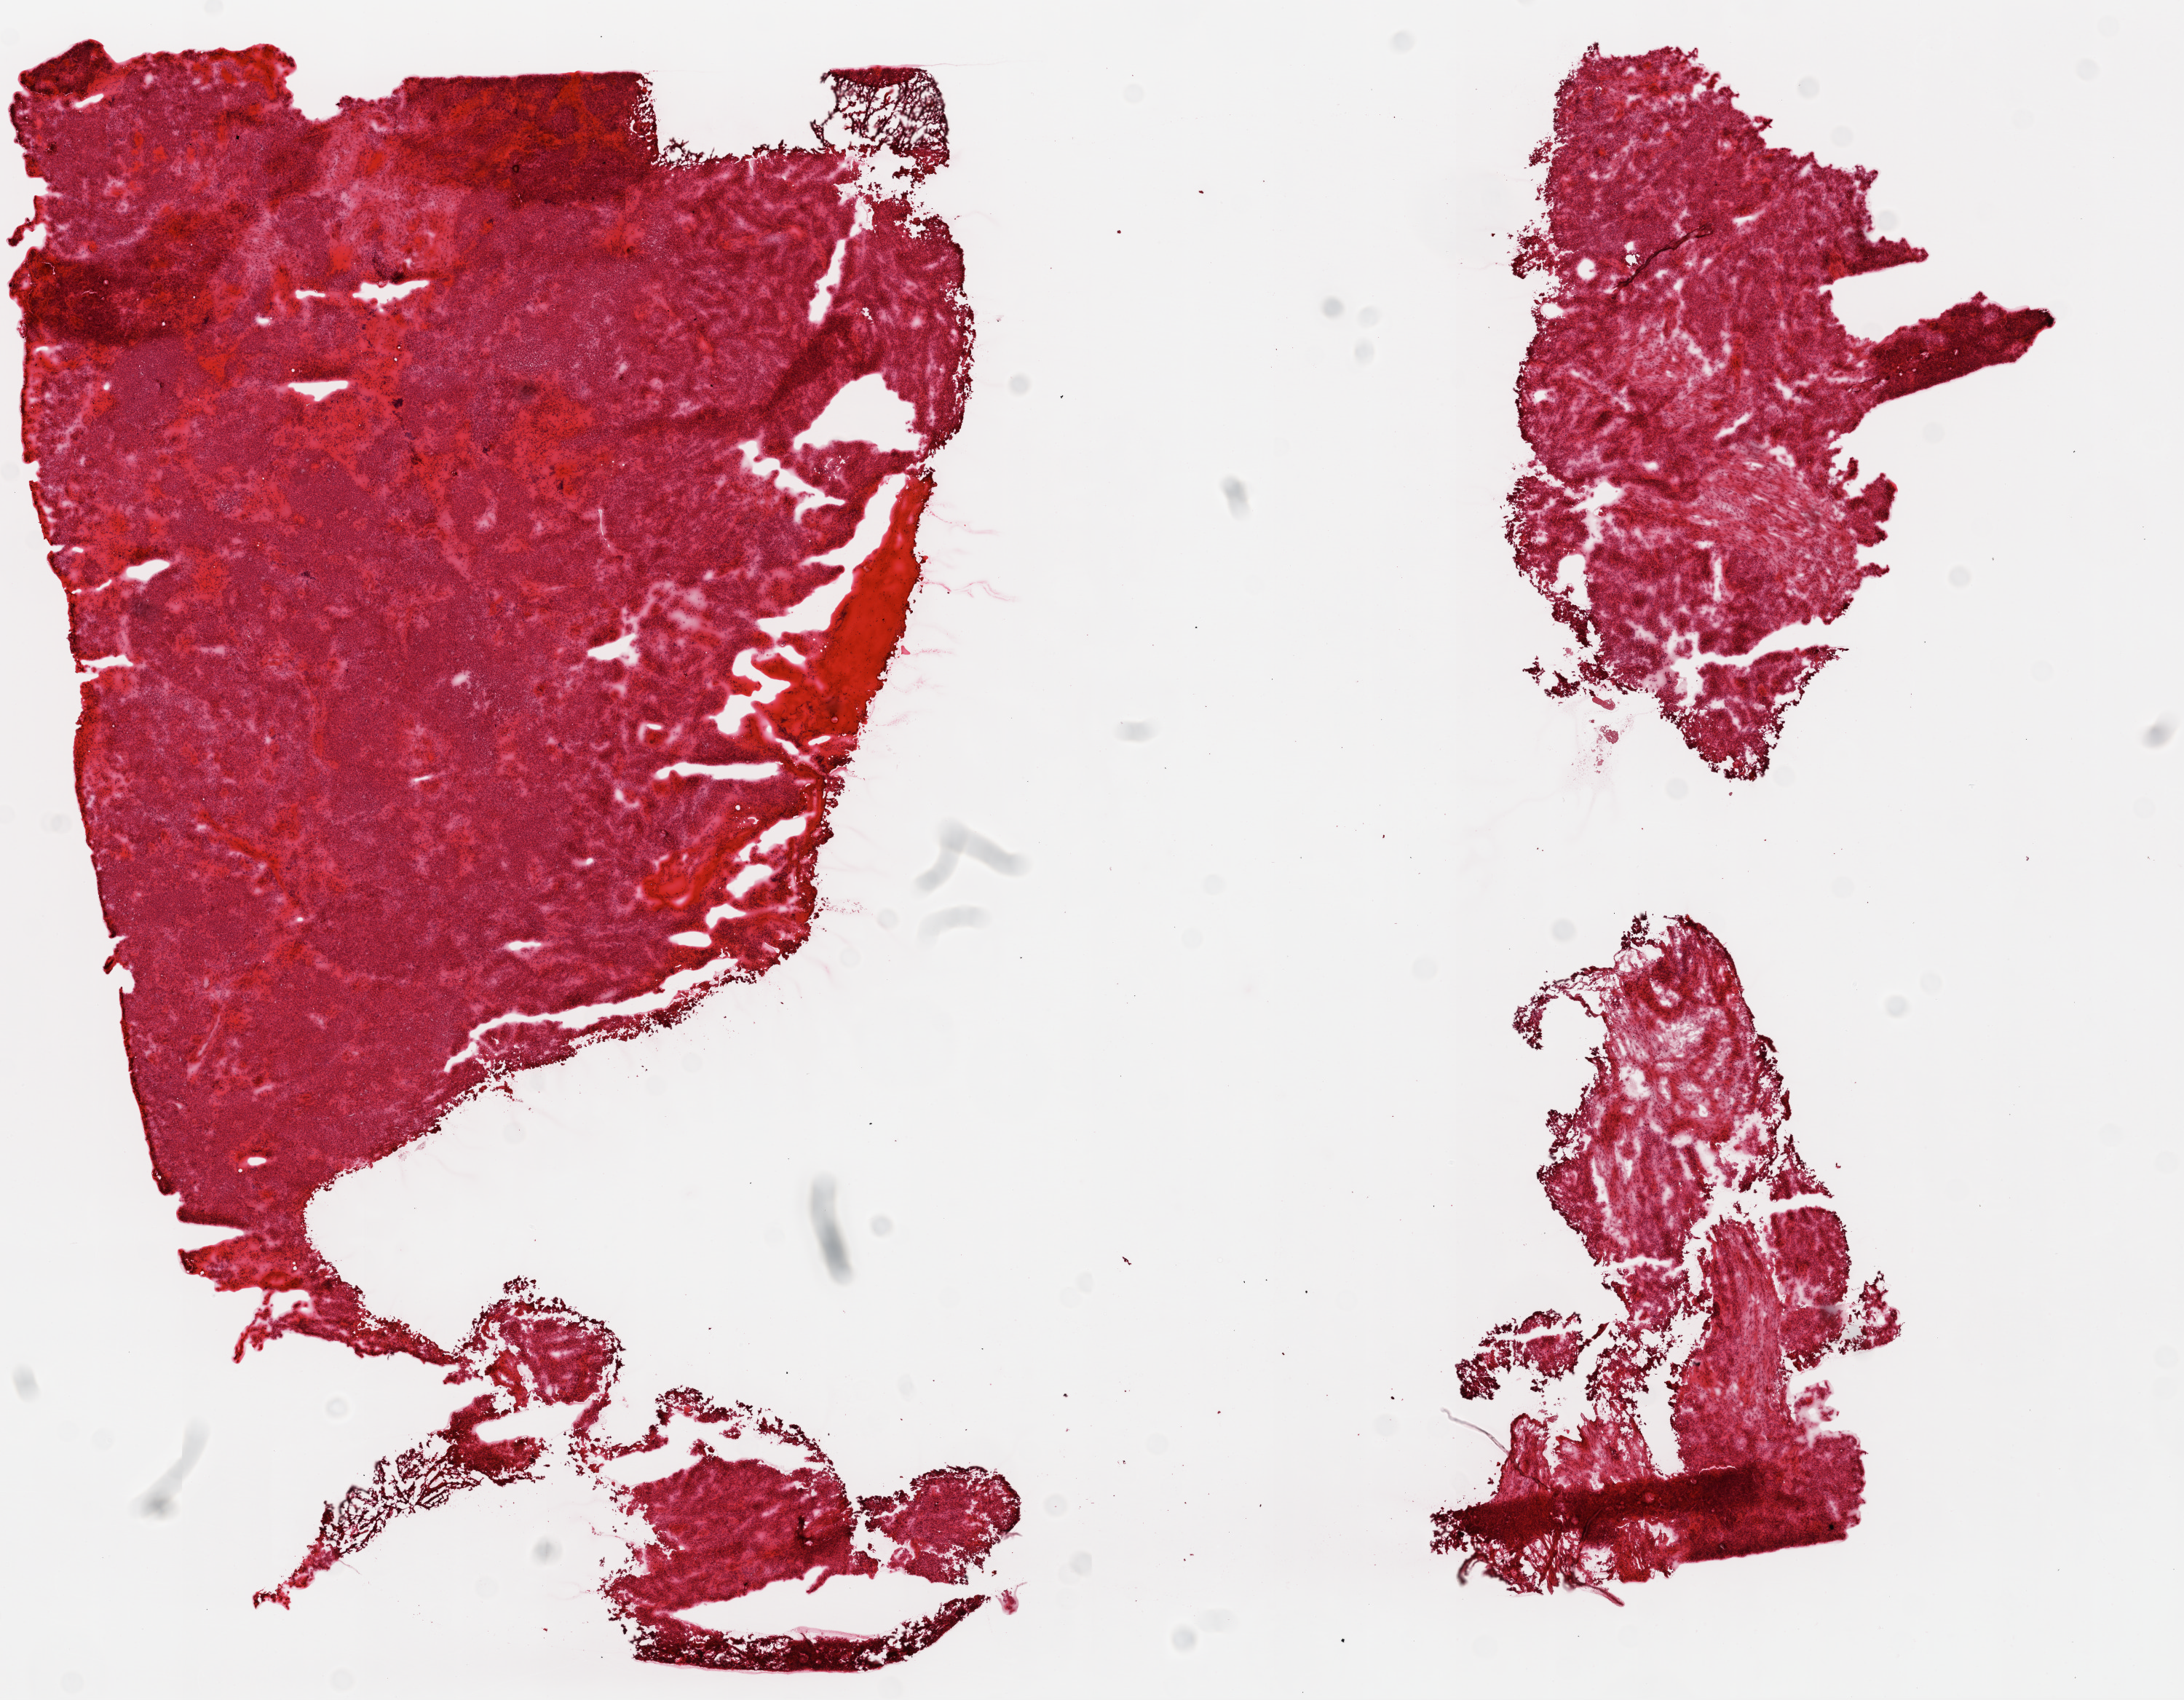
Whole-slide histology image, H&E, shown as a low-resolution overview of the whole scanned area (about 12.0 x 9.4 mm); frozen section from the top of the tissue portion; primary tumour sample from the ovary. Patient: female, age at initial diagnosis 54 years. Histologic grade: G3 (poorly differentiated). Composition of this section per pathologist review: tumour cells 95%, tumour nuclei 95%, normal cells 0%, stromal cells 4%, necrosis 1%.
* pathologic diagnosis: Serous cystadenocarcinoma, NOS
* laterality: bilateral
* FIGO stage: IIIB